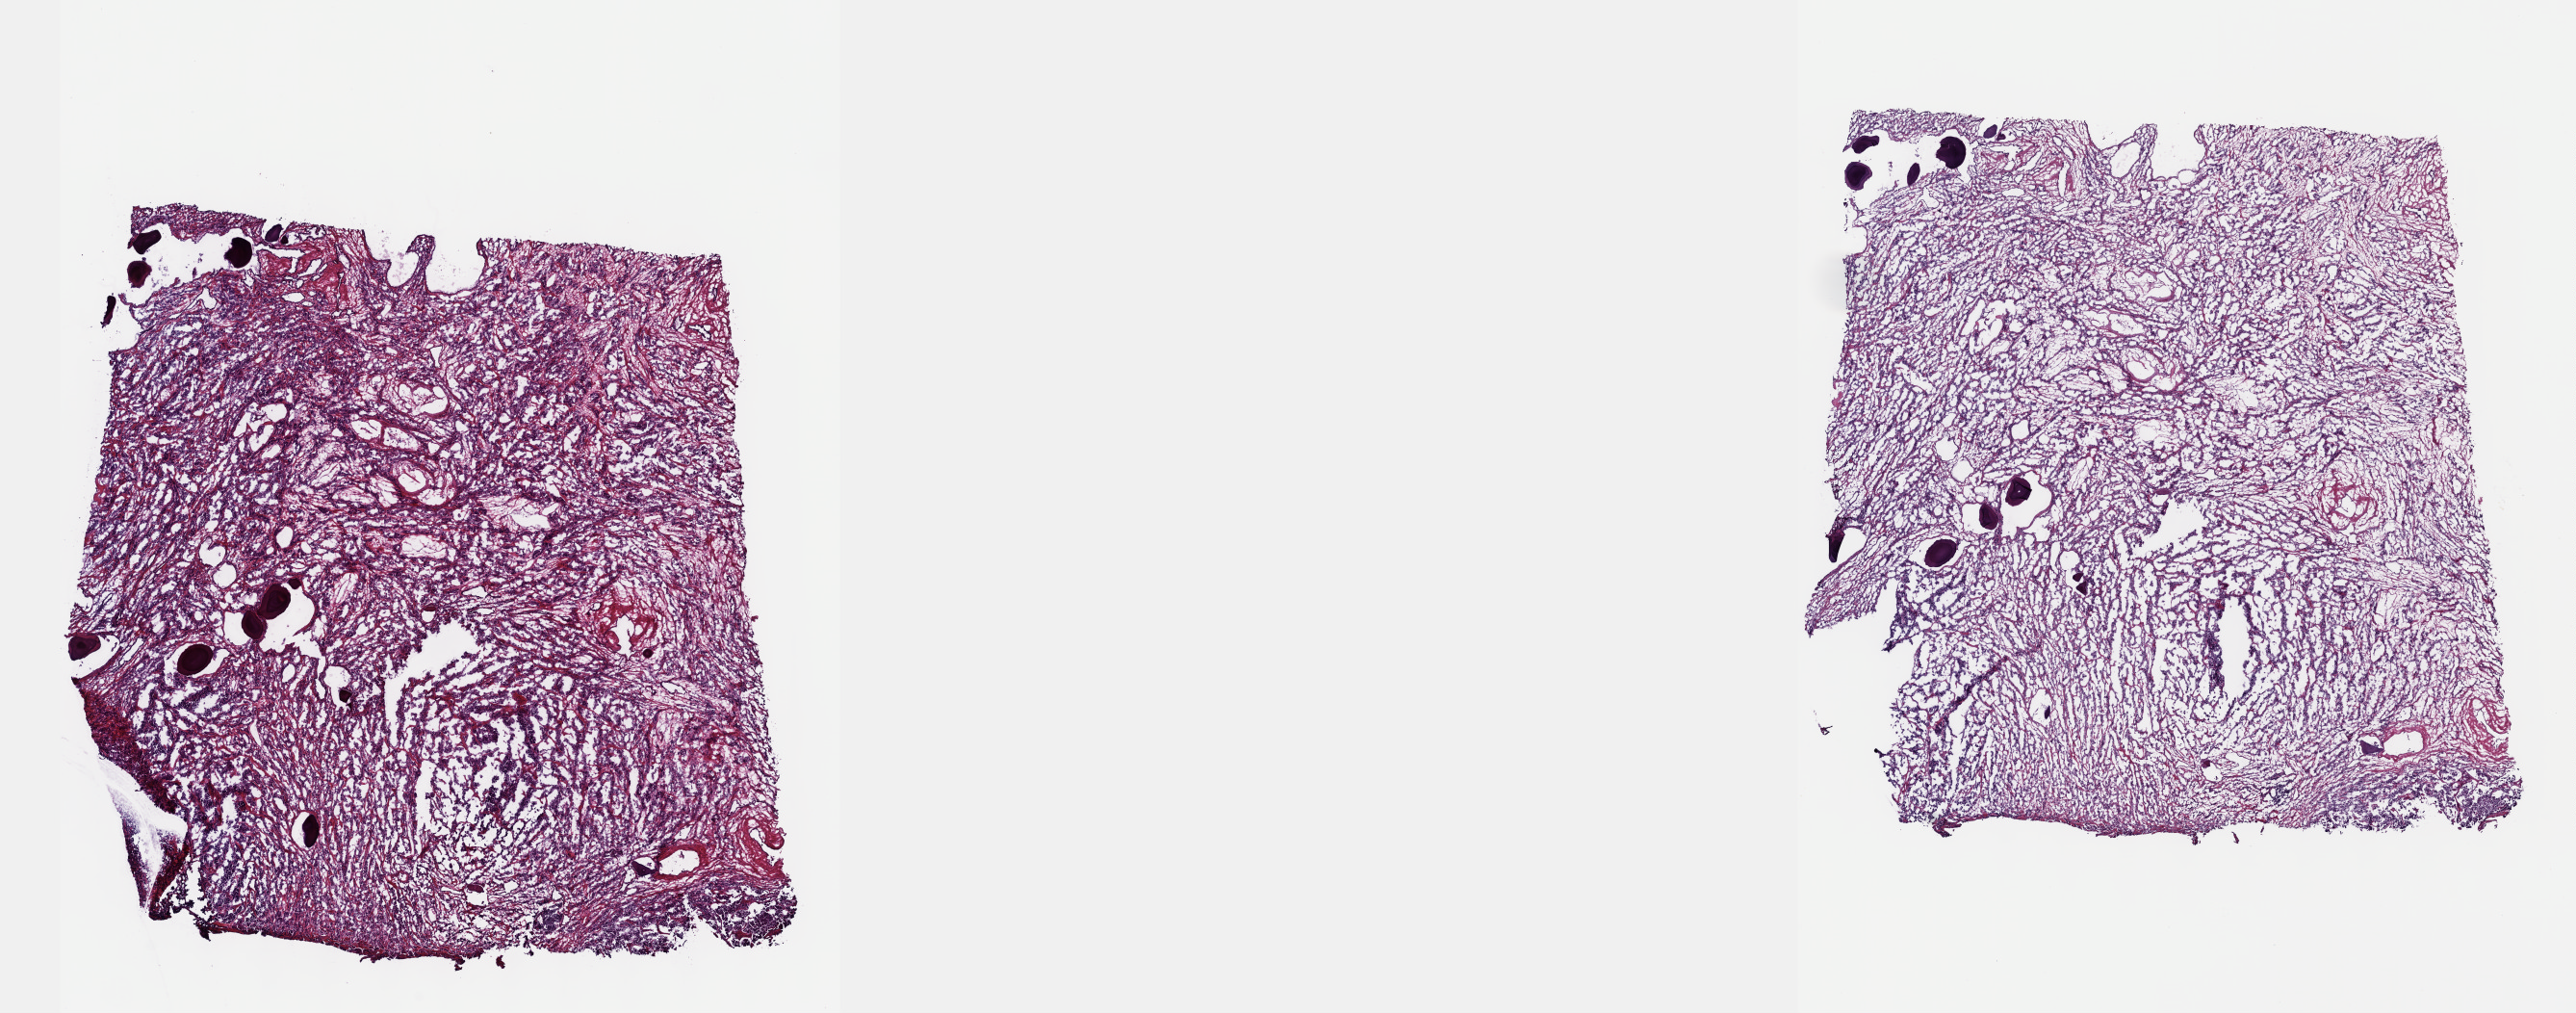
Digitized H&E tissue section (whole slide) — a low-resolution overview of the entire scanned area, about 21.6 x 8.5 mm (from a 40x scan). Frozen section. Primary tumour sample from the prostate. Male, age 72 years at initial diagnosis. Gleason score: 9 (5+4). Slide review estimates, as recorded: tumour cells 80%, tumour nuclei 80%, normal cells 2%, stromal cells 18%, necrosis 0%. Infiltration values recorded for this section: lymphocyte infiltration 2%, monocyte infiltration 1%, neutrophil infiltration 1%.
- lymph nodes positive (case pathology): 0 of 9 examined
- histologic diagnosis: Adenocarcinoma, NOS
- laterality: right